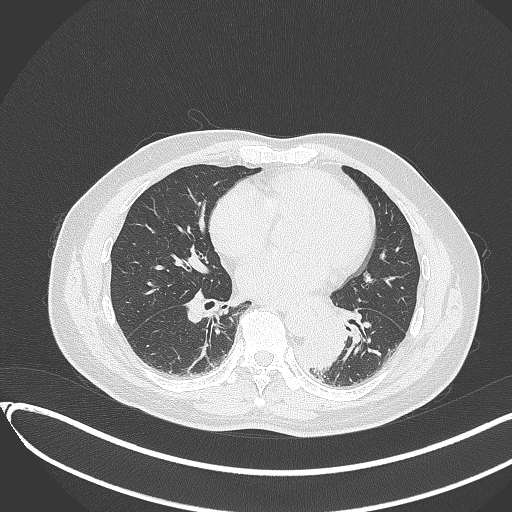
Chest CT, one axial slice. Slice 145 of 417 in the series (ordered by position). 120 kVp. Lung window (W 1500 / L -600 HU). 1 mm slice thickness. 512 × 512 image matrix, field of view 400 × 400 mm. Male patient, age 54 years. From the clinical record (not read from this slice): clinical TNM (as recorded): T3 N0 M0.
Structures marked on this image (rectangle marked by the reading radiologist):
- lung tumour (recorded histology: squamous cell carcinoma): bounding box (x1, y1, x2, y2) in pixels: (297, 327, 344, 371)